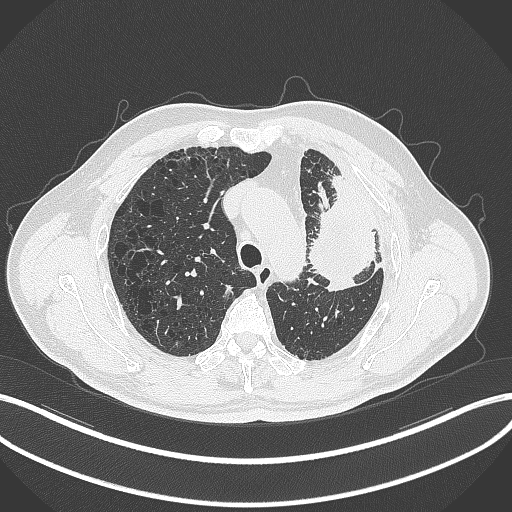
Chest CT, one axial slice; position 235 of 297 along the scan axis; 120 kVp; lung window (W 1500 / L -600 HU); 512 × 512 image matrix, field of view 400 × 400 mm. Patient: male, 68 years. From the clinical record (not read from this slice): clinical TNM (as recorded): T3 N3 M1.
Outlined on this slice (bounding box drawn by a radiologist):
- lung tumour (recorded histology: adenocarcinoma): bounding box (x1, y1, x2, y2) in pixels: (306, 161, 380, 298)